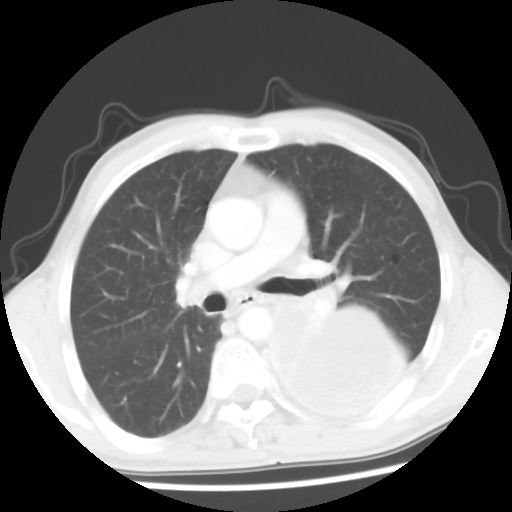
Chest CT, one axial slice; slice 34 of 56 in the series (ordered by position); 120 kVp; lung window (W 1500 / L -600 HU); 5 mm slice thickness; 512 × 512 image matrix. Male patient, age 60 years. Case-level facts recorded for this patient, not image findings: clinical TNM (as recorded): T4 N0 M0.
Outlined on this slice (bounding box drawn by a radiologist):
- lung tumour (recorded histology: squamous cell carcinoma): bounding box (x1, y1, x2, y2) in pixels: (260, 300, 410, 424)